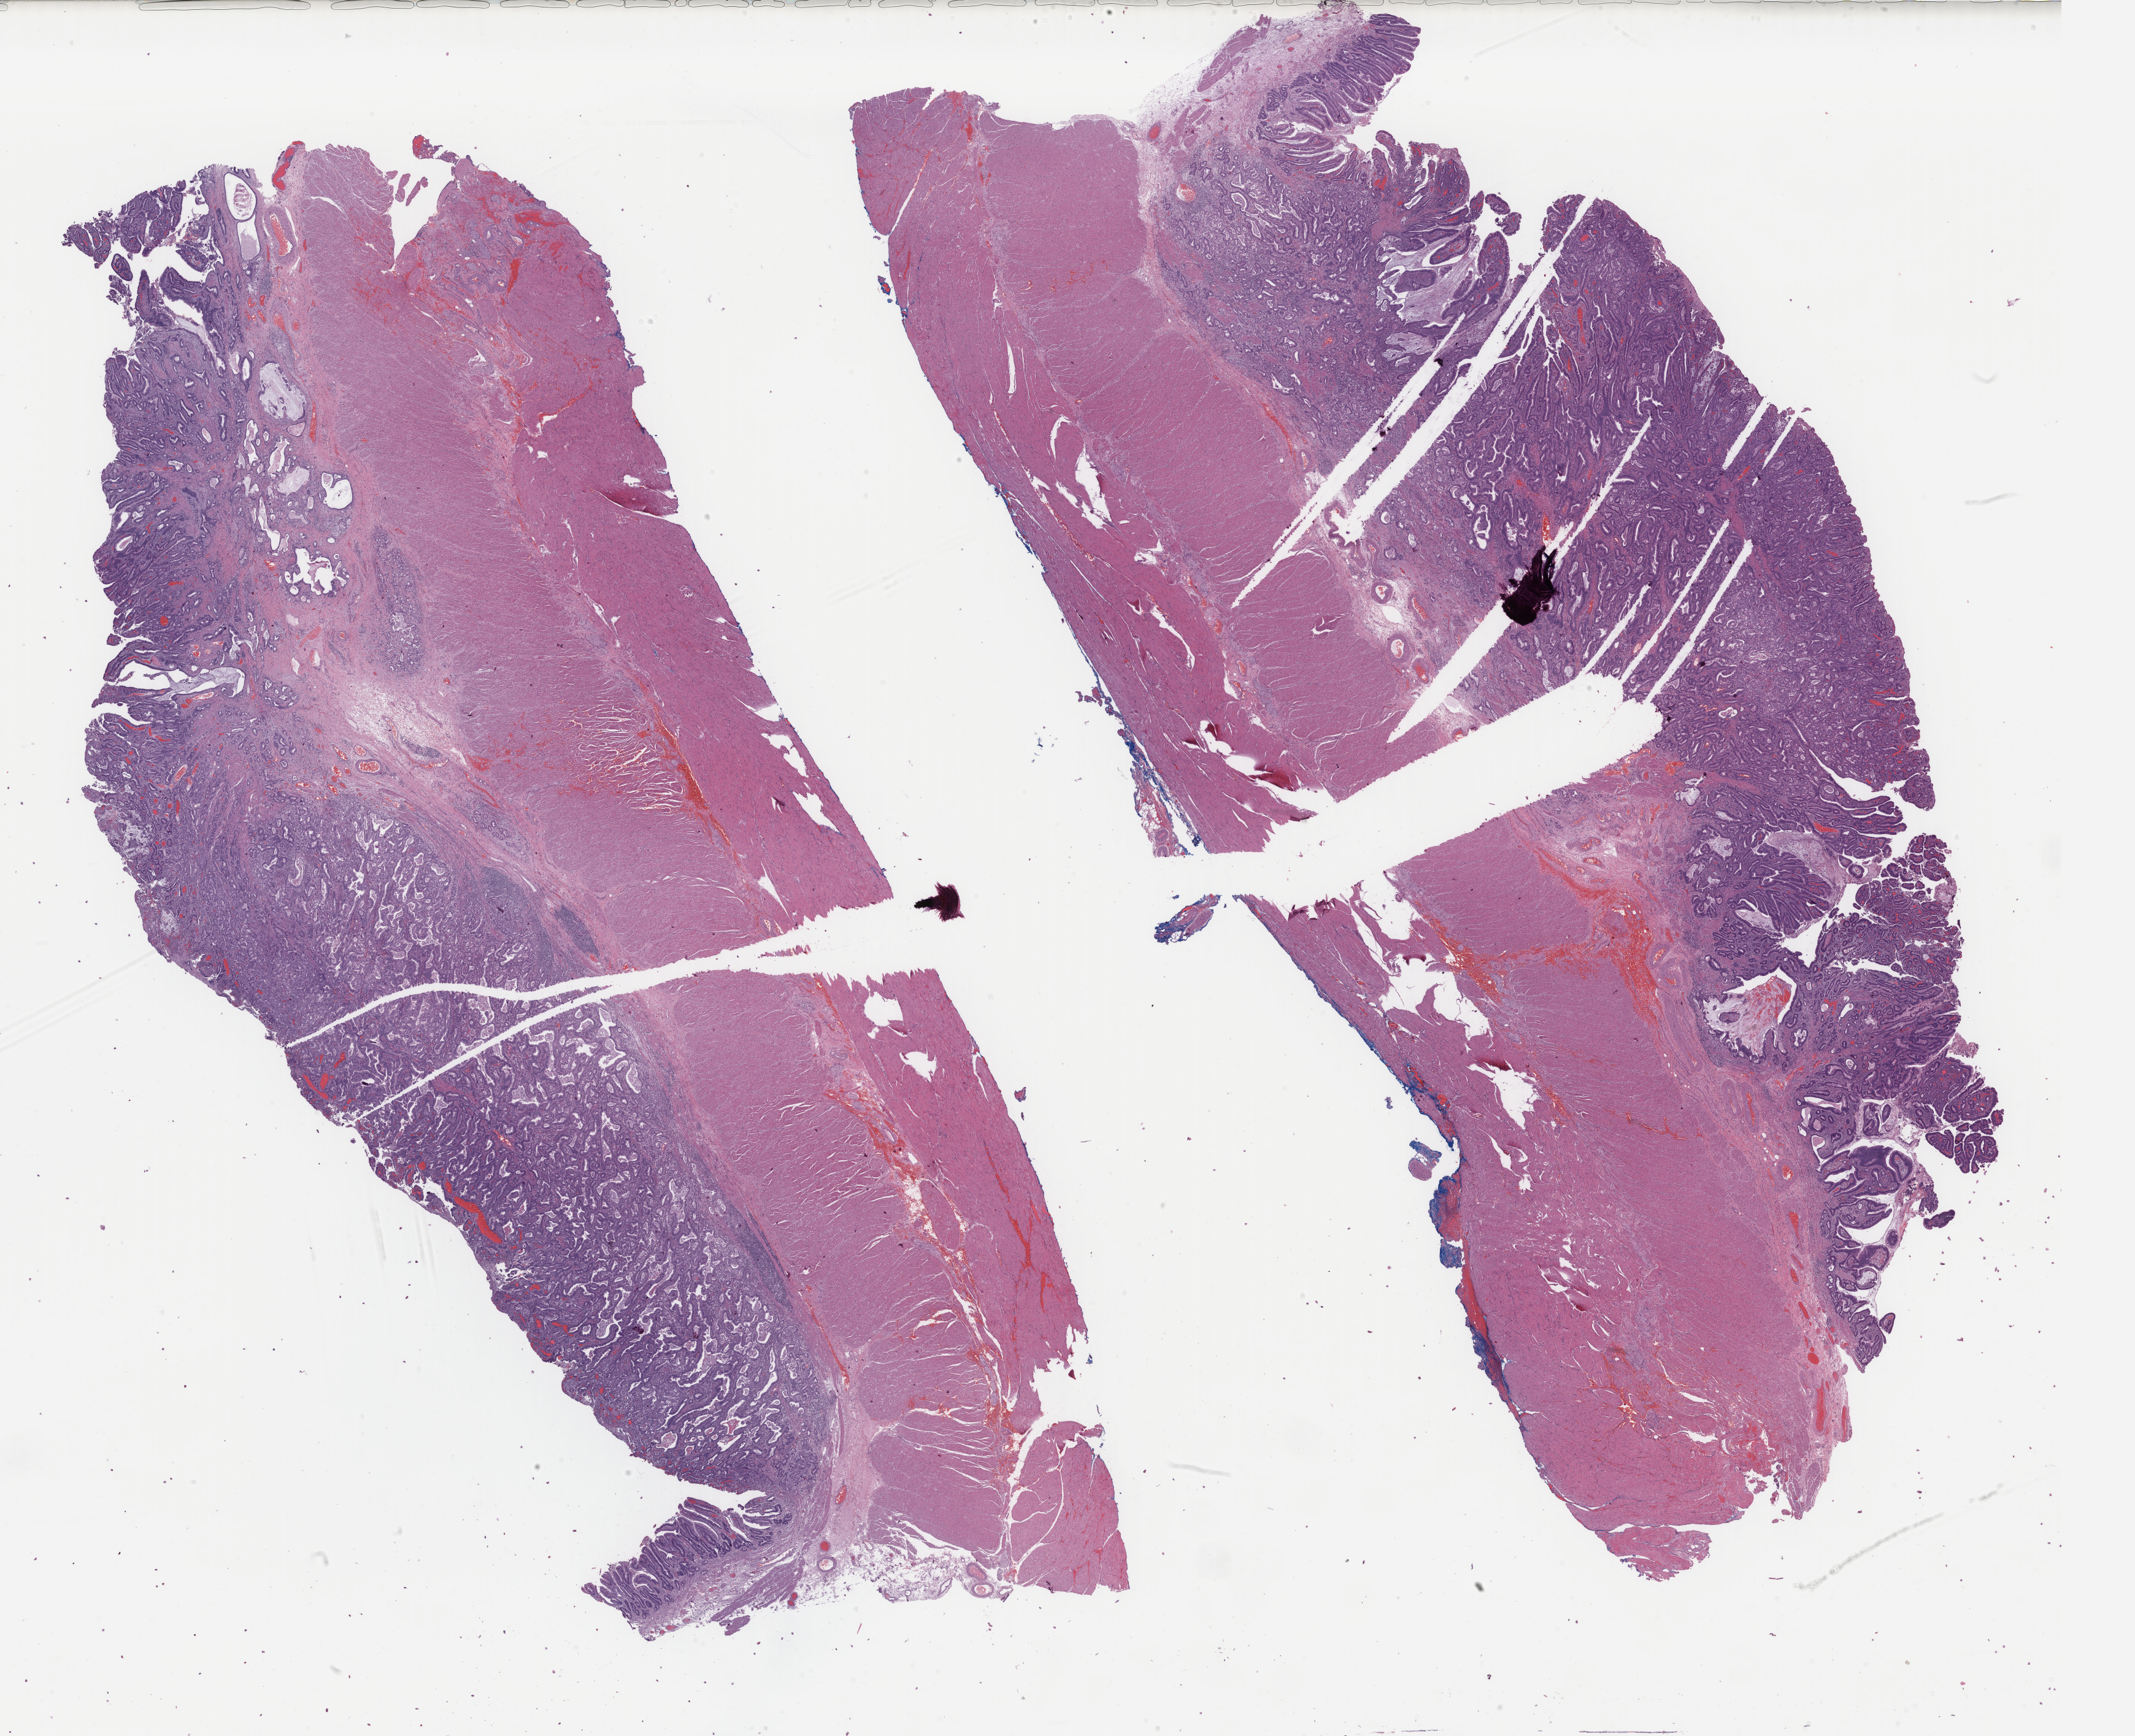
Whole-slide histology image, H&E-stained — shown as a low-resolution overview of the whole scanned area (about 27.6 x 22.5 mm); formalin-fixed paraffin-embedded (FFPE) diagnostic section; primary tumour sample from the esophagus. Patient: male, age at initial diagnosis 83 years. Histologic grade: GX (grade cannot be assessed).
• pathologic diagnosis: Adenocarcinoma, NOS (lower third of esophagus)
• AJCC pathologic stage: IA (7th edition)
• TNM: T1 N0 MX